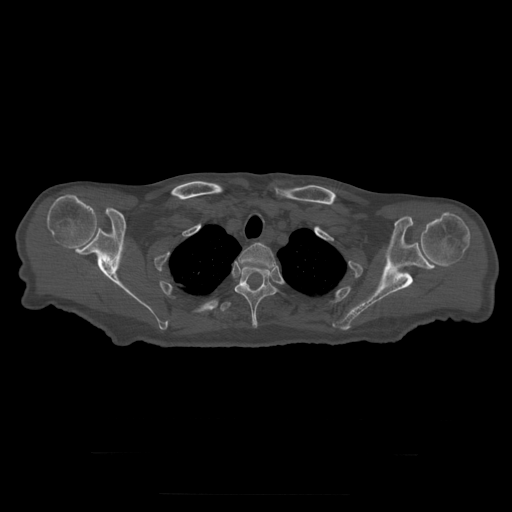
CT including the spine, one axial slice. Position 260 of 397 along the scan axis. 120 kVp. Bone window (W 1800 / L 400 HU). 1.25 mm slice thickness. 512 × 512 image matrix, field of view 510 × 510 mm. Patient age 73 years. Case-level facts recorded for this patient, not image findings: primary cancer: prostate.
Annotated regions visible in this slice (semi-automatic segmentation, software-assisted and operator-edited):
- T2 vertebra: bounding box <238,243,277,269> (left, top, right, bottom; pixels)
- T3 vertebra: <235,266,277,329>
- T4 vertebra: <220,285,263,312>